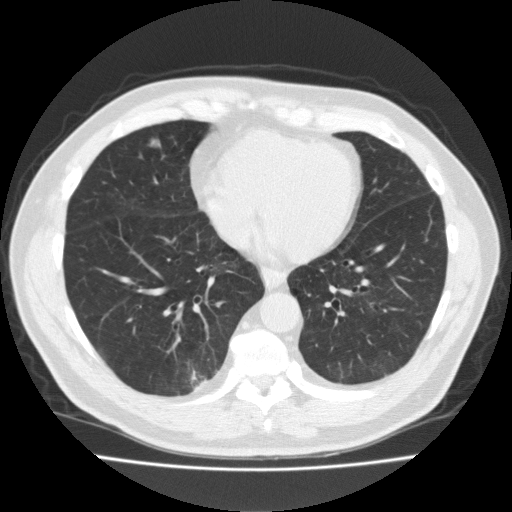
Low-dose screening chest CT, one axial slice; slice 66 of 184 in the series (ordered by position); 120 kVp; lung window (W 1500 / L -600 HU); 512 × 512 image matrix.
Structures marked on this image (expert manual segmentation):
- lesion 1 (tumor, middle lobe of right lung): bounding box [x1, y1, x2, y2] px = [151, 140, 160, 147]